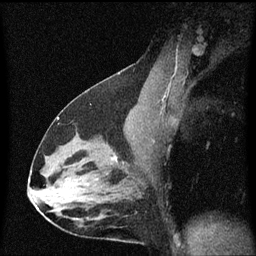
Breast MRI (dynamic contrast-enhanced), one sagittal slice. Position 34 of 60 along the scan axis. Dynamic contrast-enhanced series, image 2 of 3 at this slice position (ordered by acquisition). 1.5 T. TE 4.2 ms, TR 8.4 ms. 256 × 256 image matrix, field of view 200 × 200 mm. Female patient, age 38 years. From the clinical record (not read from this slice): setting: breast cancer imaged before/during neoadjuvant chemotherapy; receptor status: HR-positive, HER2-negative.
Annotated regions visible in this slice (semi-automatic segmentation, software-assisted and operator-edited):
- analysis volume of interest (the breast-tissue region the enhancement analysis was run in; not a lesion): bounding box <94,138,141,185> (left, top, right, bottom; pixels)
- tumour enhancement mask (voxels above the 70 % enhancement threshold inside the analysis volume of interest): <115,156,117,159>